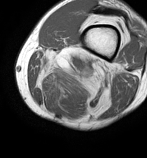
MRI of an extremity soft-tissue mass, one axial slice. Position 20 of 86 along the scan axis. MR volume resampled by the dataset authors to the PET/CT grid (not the native acquisition matrix). 3.27 mm slice thickness. 147 × 158 image matrix, field of view 144 × 154 mm. Male patient. From the clinical record (not read from this slice): histological type: undifferentiated pleomorphic liposarcoma; grade: high; site of the primary tumour: left thigh.
Structures marked on this image (expert contour drawn on MRI and transferred to this co-registered scan by the dataset authors):
- gross tumour volume including surrounding oedema: bounding box <35,46,120,114> (left, top, right, bottom; pixels)